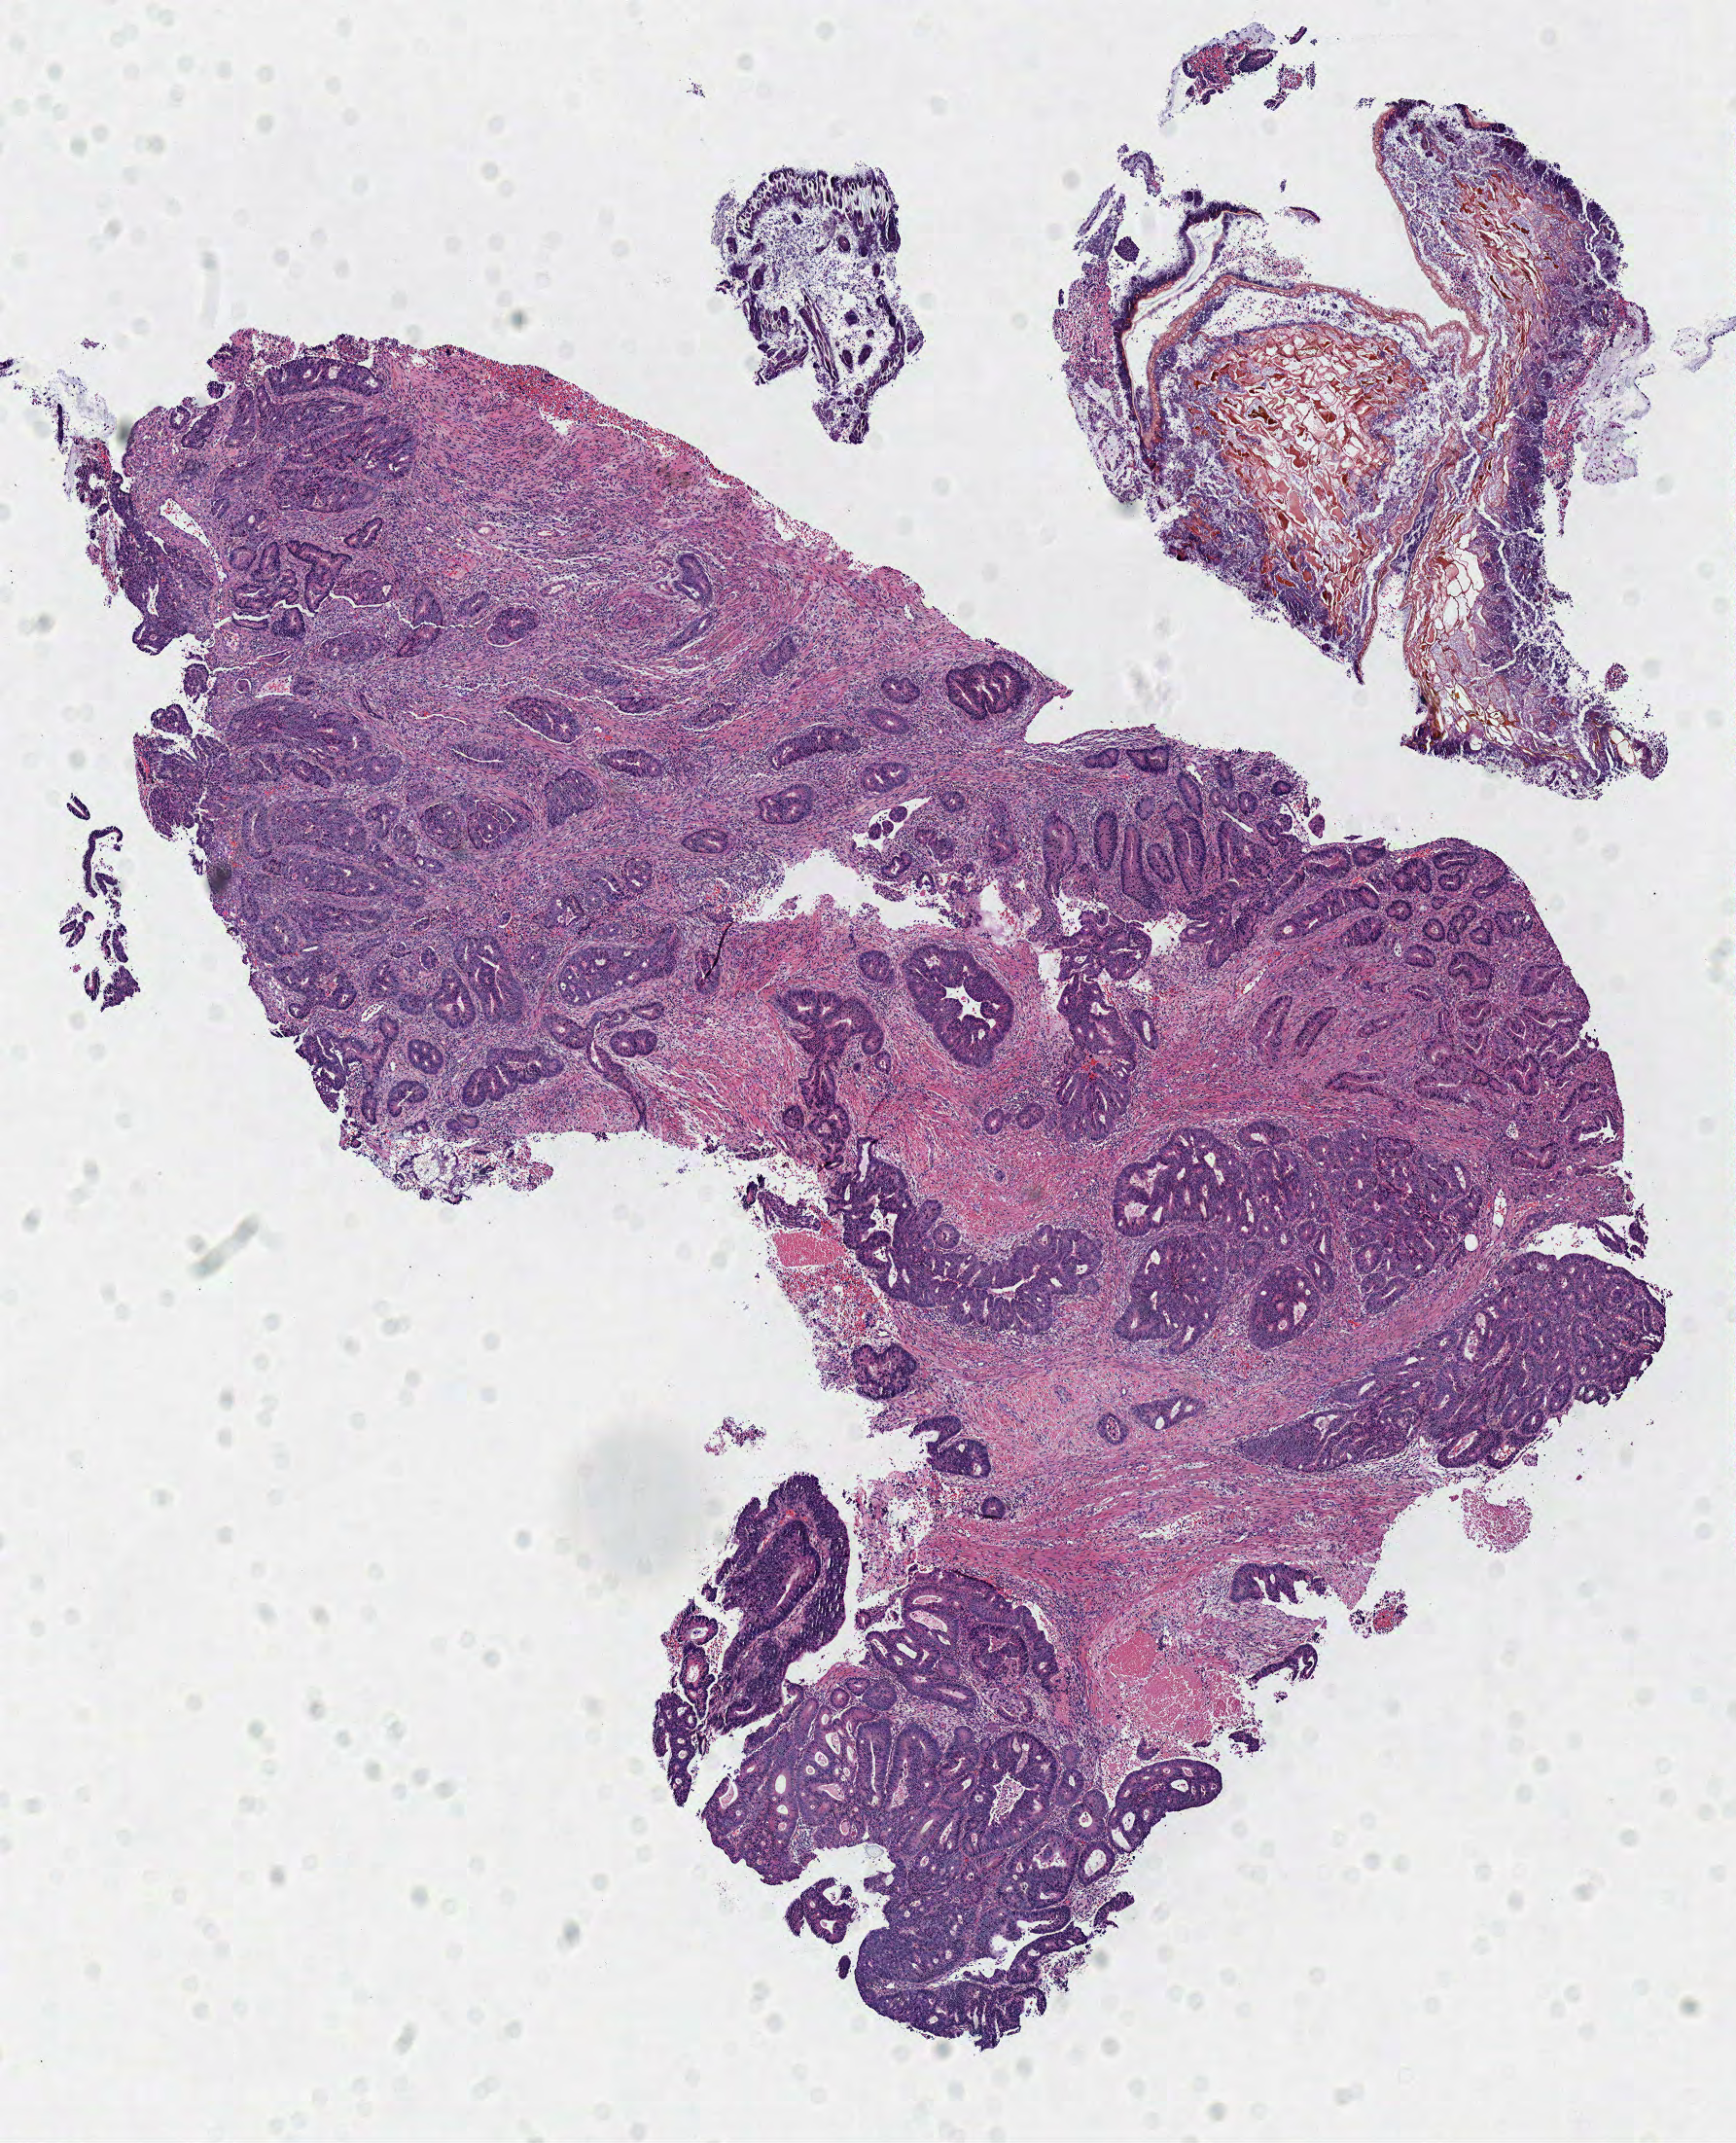
Whole-slide histology image, Hematoxylin and eosin (H&E) stained — low-resolution overview of the scanned area, about 7.0 x 8.7 mm; frozen section from the top of the tissue portion; primary tumour sample from the colon. Male patient; age at initial diagnosis 62 years. Composition of this section per pathologist review: tumour cells 99%, tumour nuclei 75%, normal cells 0%, stromal cells 0%, necrosis 1%. Inflammatory infiltration, as recorded: lymphocyte infiltration 10%, monocyte infiltration 0%, neutrophil infiltration 10%.
Pathologic diagnosis: Adenocarcinoma, NOS (descending colon). AJCC pathologic stage: IIA.